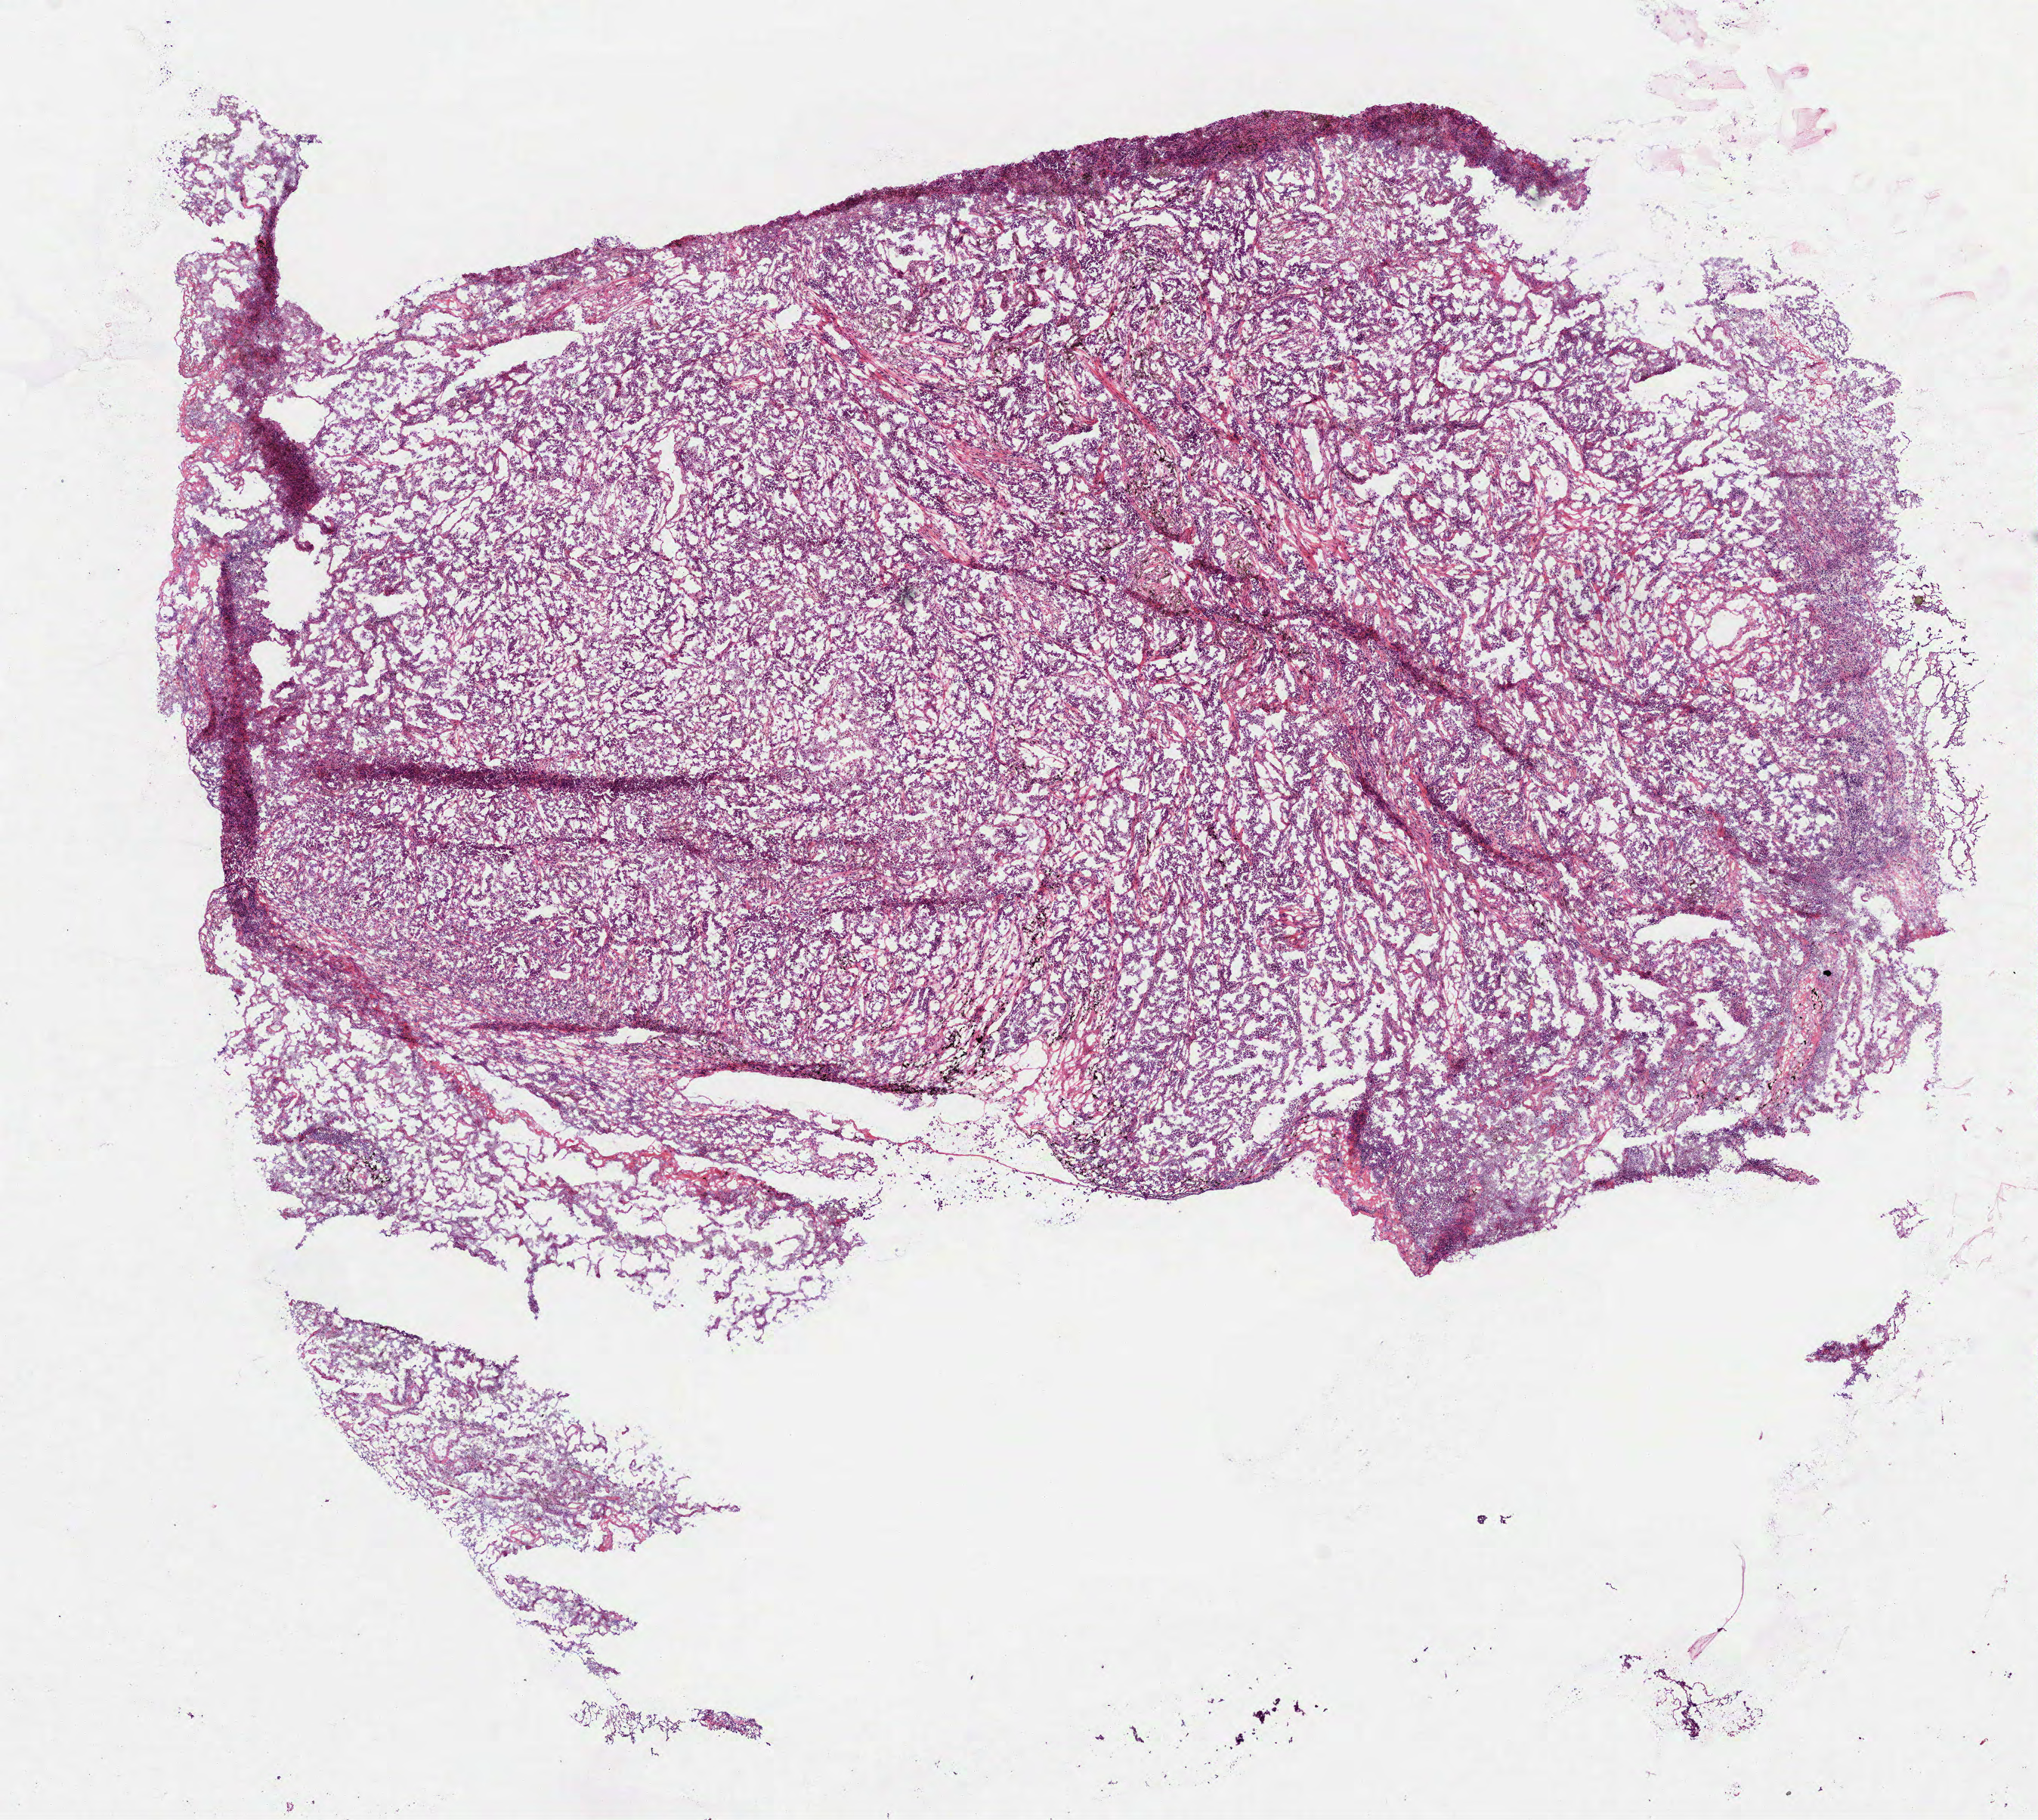
Whole-slide histology image, Hematoxylin and eosin (H&E) stained, a low-resolution overview of the entire scanned area, about 10.9 x 9.7 mm (slide scanned at 40x). Frozen section. Lung, primary tumour sample. Patient: male, age at initial diagnosis 60 years. Composition of this section per pathologist review: tumour cells 80%, tumour nuclei 60%, normal cells 3%, stromal cells 10%, necrosis 7%. Inflammatory infiltration, as recorded: lymphocyte infiltration 1%, monocyte infiltration 5%, neutrophil infiltration 0%.
Laterality: right. AJCC pathologic stage: IA (7th edition). Pathologic diagnosis: Adenocarcinoma, NOS (lower lobe, lung). TNM: T1 N0 M0.